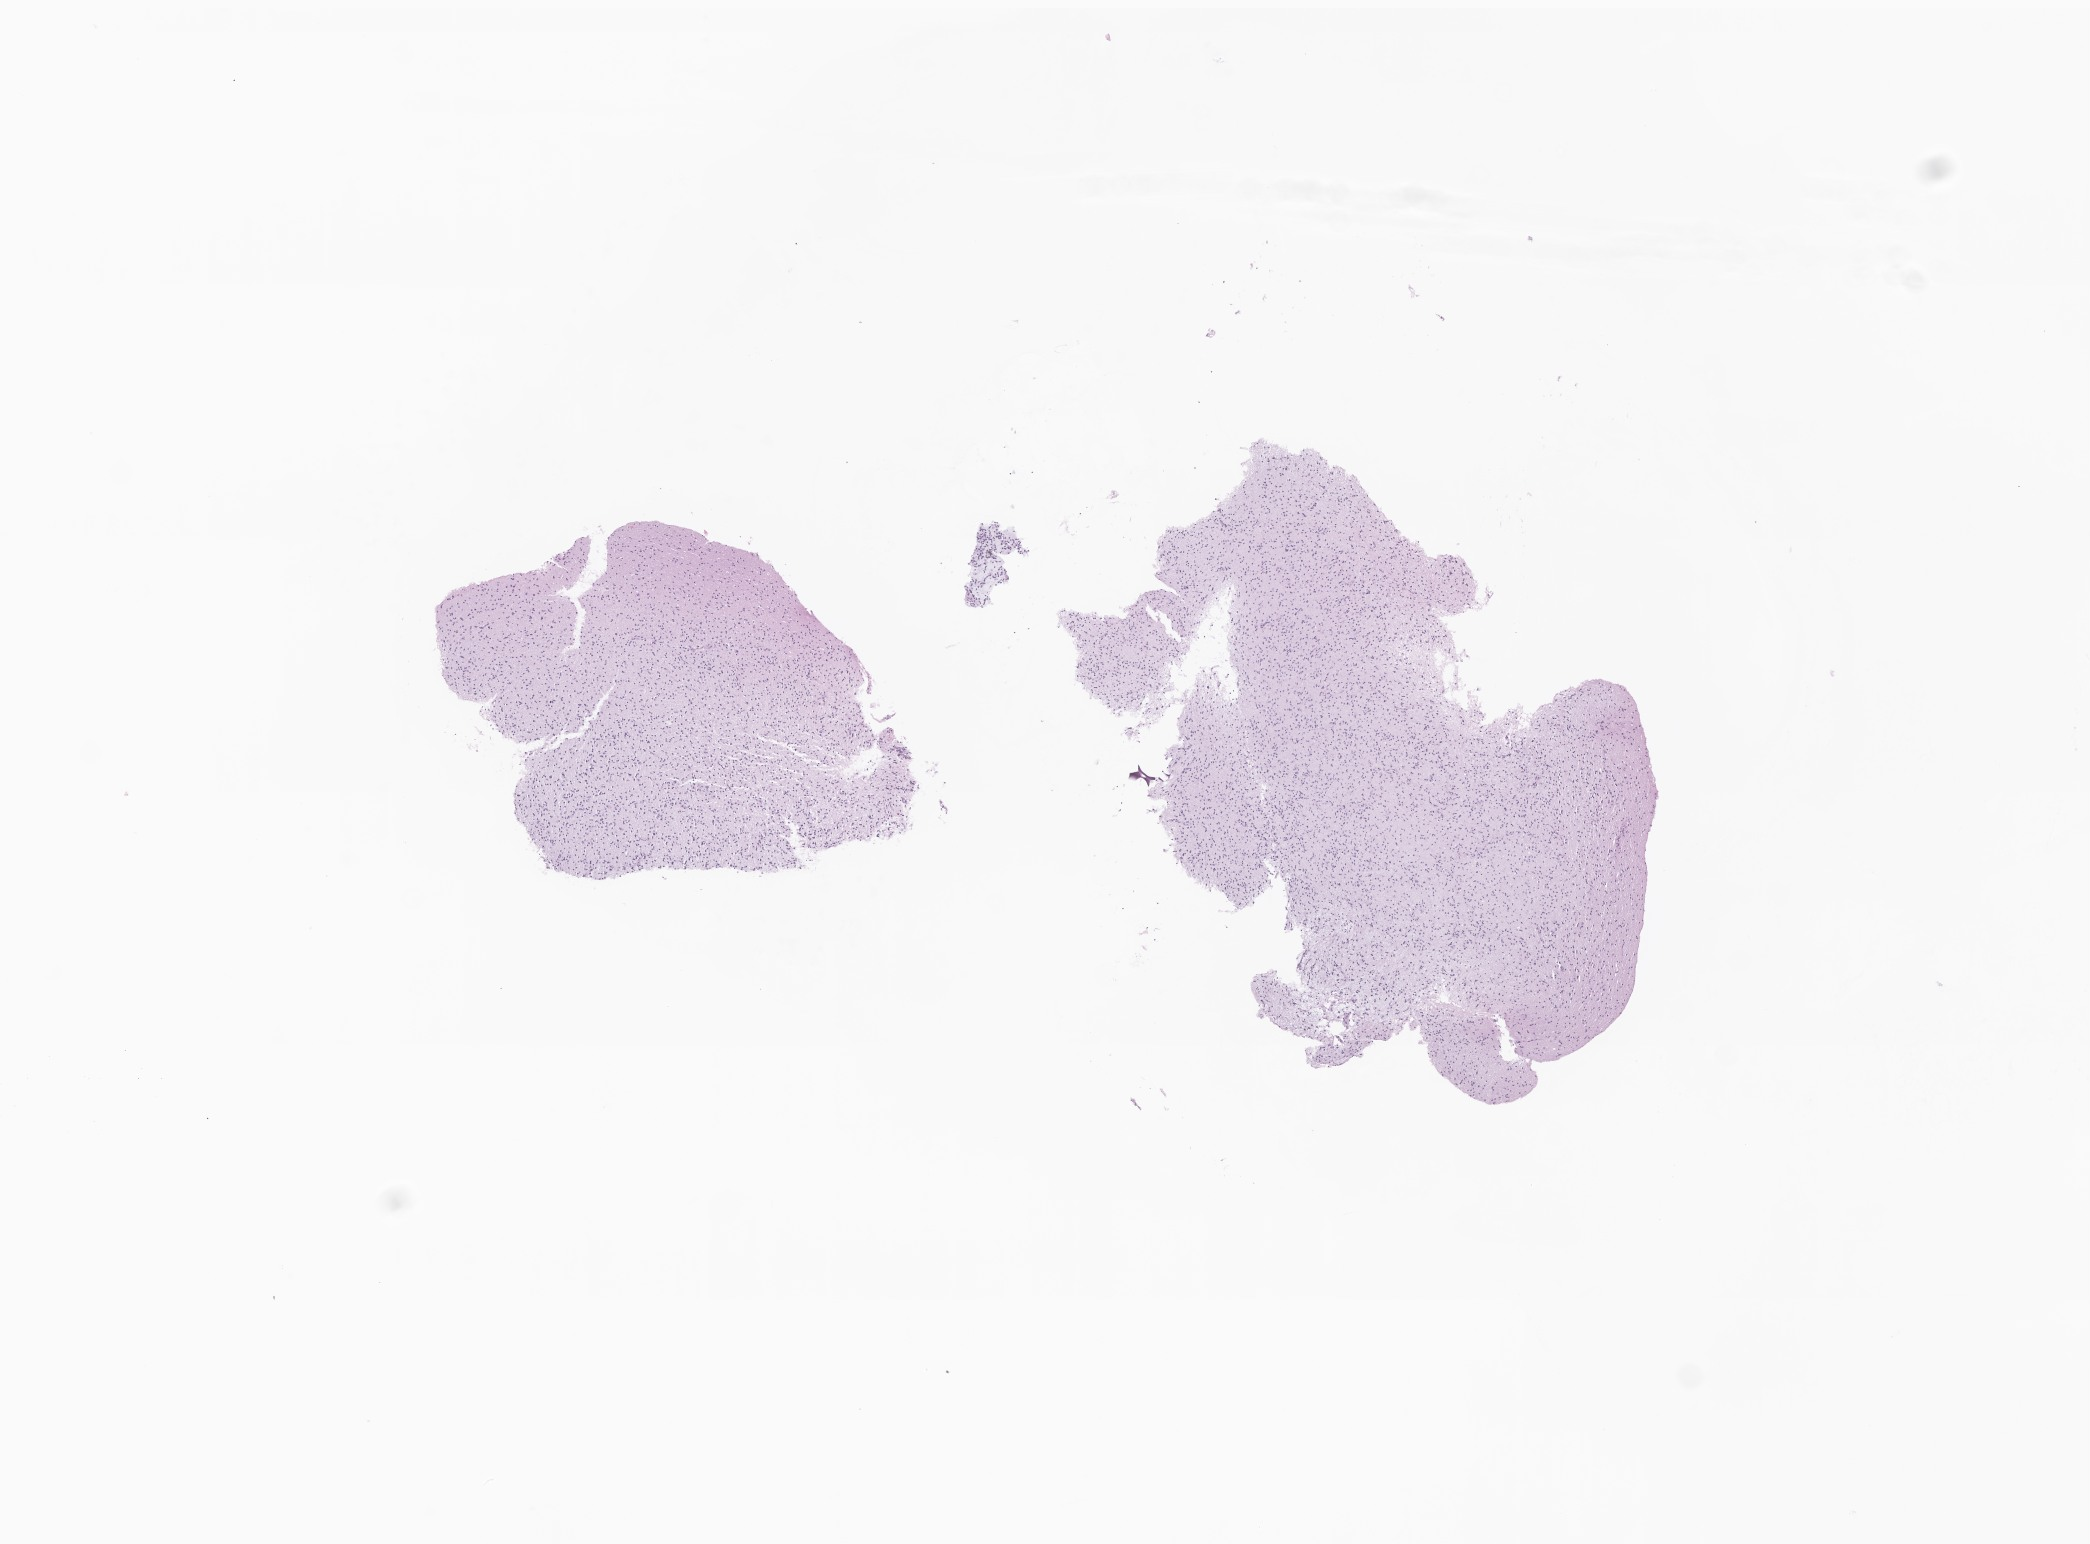
Whole-slide image, hematoxylin and eosin (H&E) stain of tumor tissue from the brain, whole scanned area (about 8.8 x 6.5 mm) shown as a low-resolution overview; FFPE section. Female patient, age 190 months (15 years 10 months).
Diagnosis: Glioma, malignant.